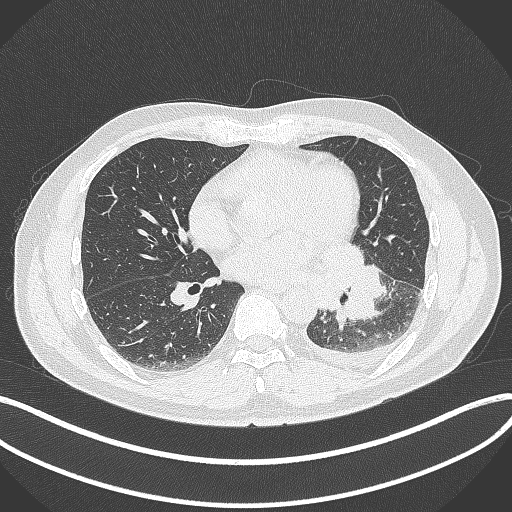
Chest CT, one axial slice. Slice 161 of 342 in the series (ordered by position). Reconstruction kernel B70f. 120 kVp. Lung window (W 1500 / L -600 HU). 1 mm slice thickness. 512 × 512 image matrix, field of view 400 × 400 mm. Male patient, age 58 years. Case-level facts recorded for this patient, not image findings: clinical TNM (as recorded): T3 N1 M1b; histopathological grade: G3.
Structures marked on this image (bounding box drawn by a radiologist):
- lung tumour (recorded histology: small cell carcinoma): bounding box (x1, y1, x2, y2) in pixels: (317, 239, 386, 326)